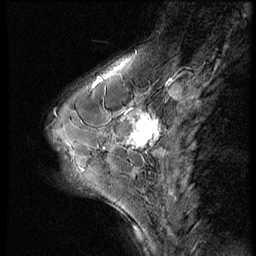
Breast MRI (dynamic contrast-enhanced), one sagittal slice; dynamic contrast-enhanced series, image 2 of 3 at this slice position (ordered by acquisition); 1.5 T; TE 4.2 ms, TR 9 ms; 256 × 256 image matrix. Patient: female, 46 years. Case-level facts recorded for this patient, not image findings: setting: breast cancer imaged before/during neoadjuvant chemotherapy; receptor status: HER2-positive.
Structures marked on this image (semi-automatic segmentation, software-assisted and operator-edited):
- analysis volume of interest (the breast-tissue region the enhancement analysis was run in; not a lesion): bounding box [x1, y1, x2, y2] px = [64, 98, 174, 182]
- tumour enhancement mask (voxels above the 140 % enhancement threshold inside the analysis volume of interest): [126, 111, 160, 149]